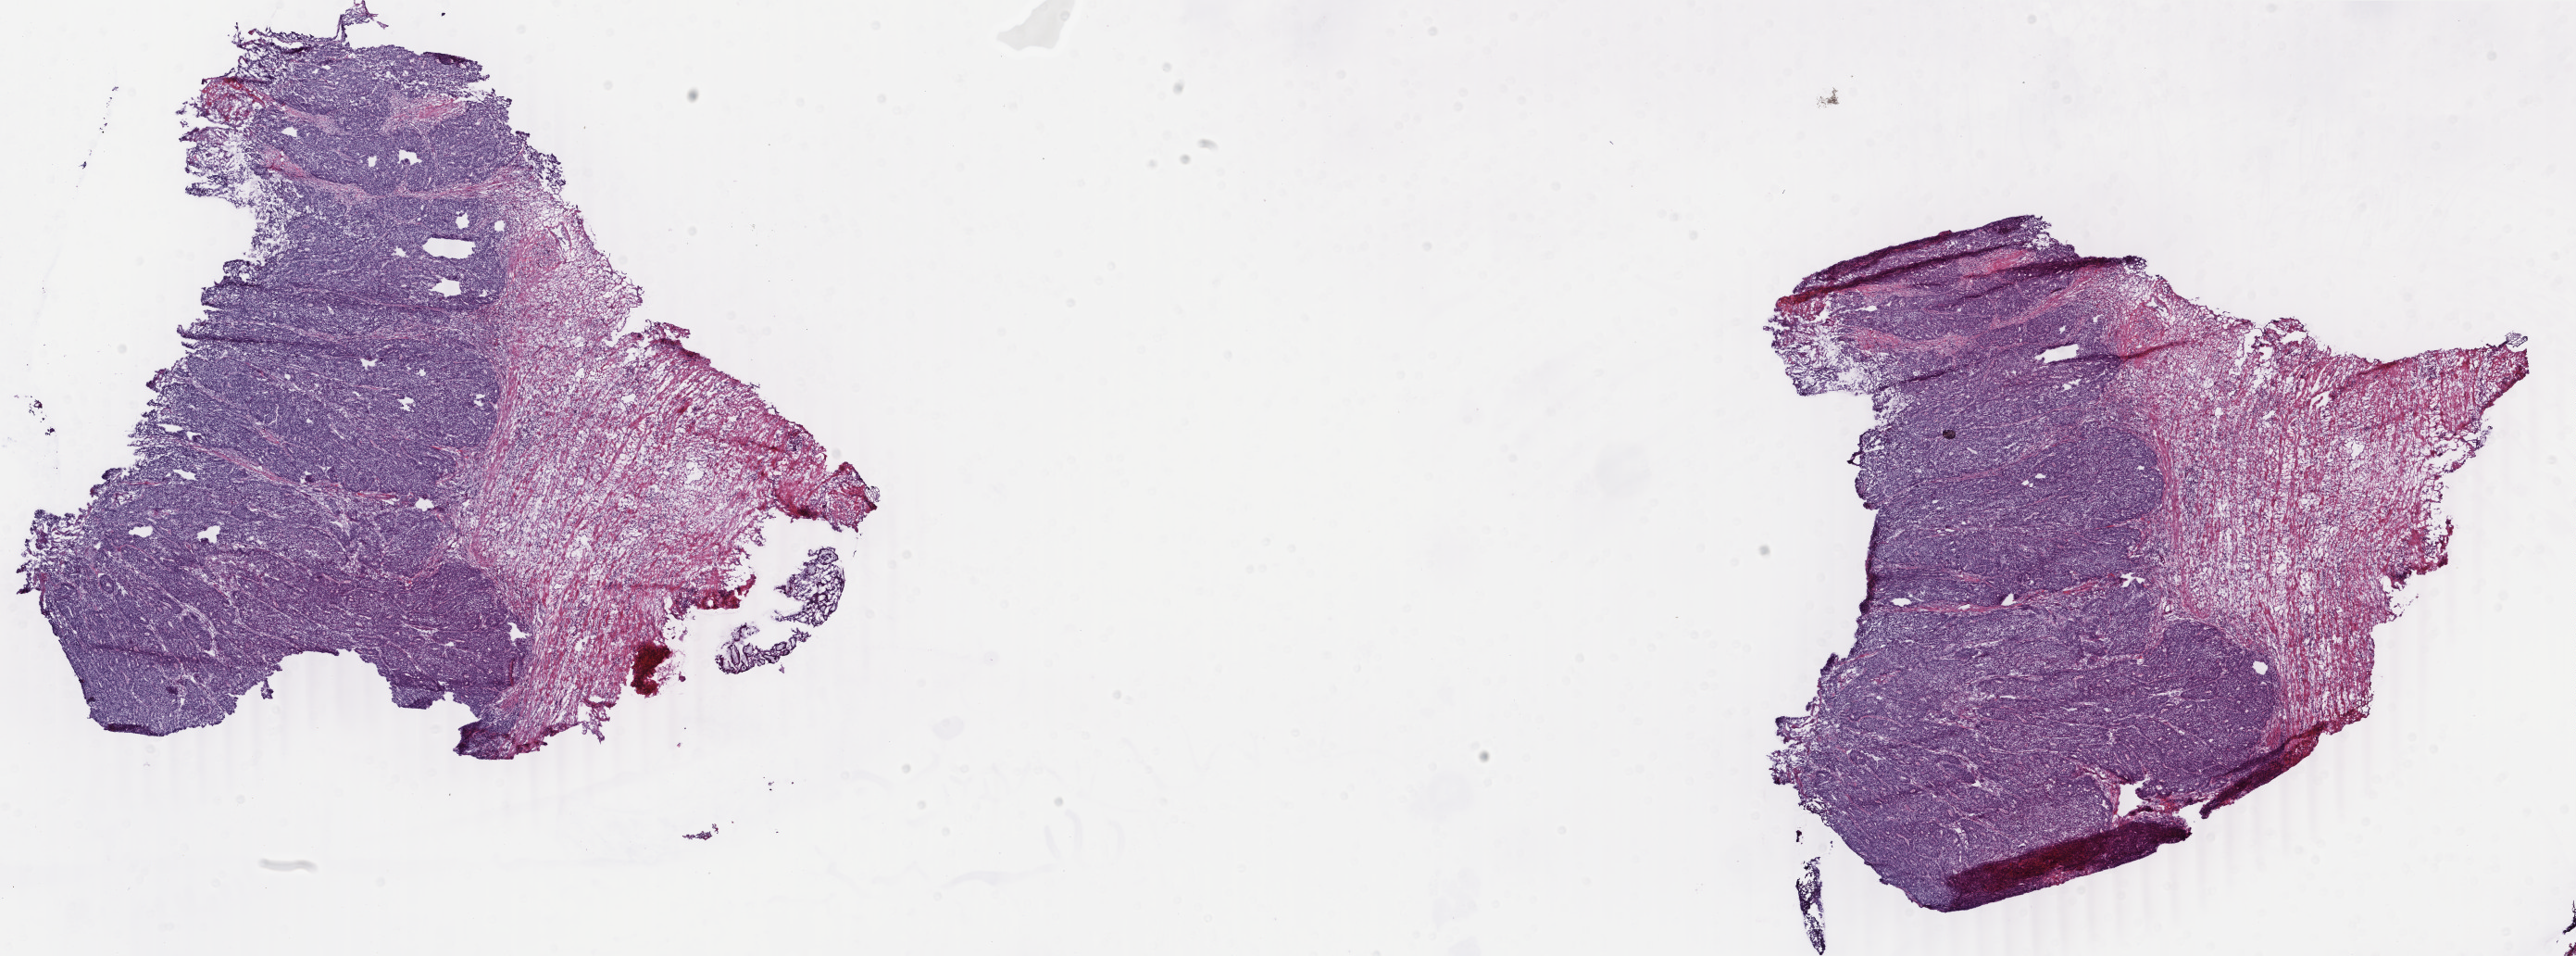
Whole-slide histology image, H&E — low-resolution overview of the scanned area, about 22.1 x 8.2 mm, frozen section, colon, primary tumour sample. Female patient; age at initial diagnosis 46 years. Composition of this section per pathologist review: tumour cells 70%, tumour nuclei 85%, normal cells 0%, stromal cells 28%, necrosis 2%. Infiltration values recorded for this section: lymphocyte infiltration 11%, monocyte infiltration 1%, neutrophil infiltration 2%.
* diagnosis: Adenocarcinoma, NOS (transverse colon)
* lymph nodes positive (case pathology): 0 of 45 examined
* AJCC pathologic stage: IIB
* TNM: T4 N0 M0